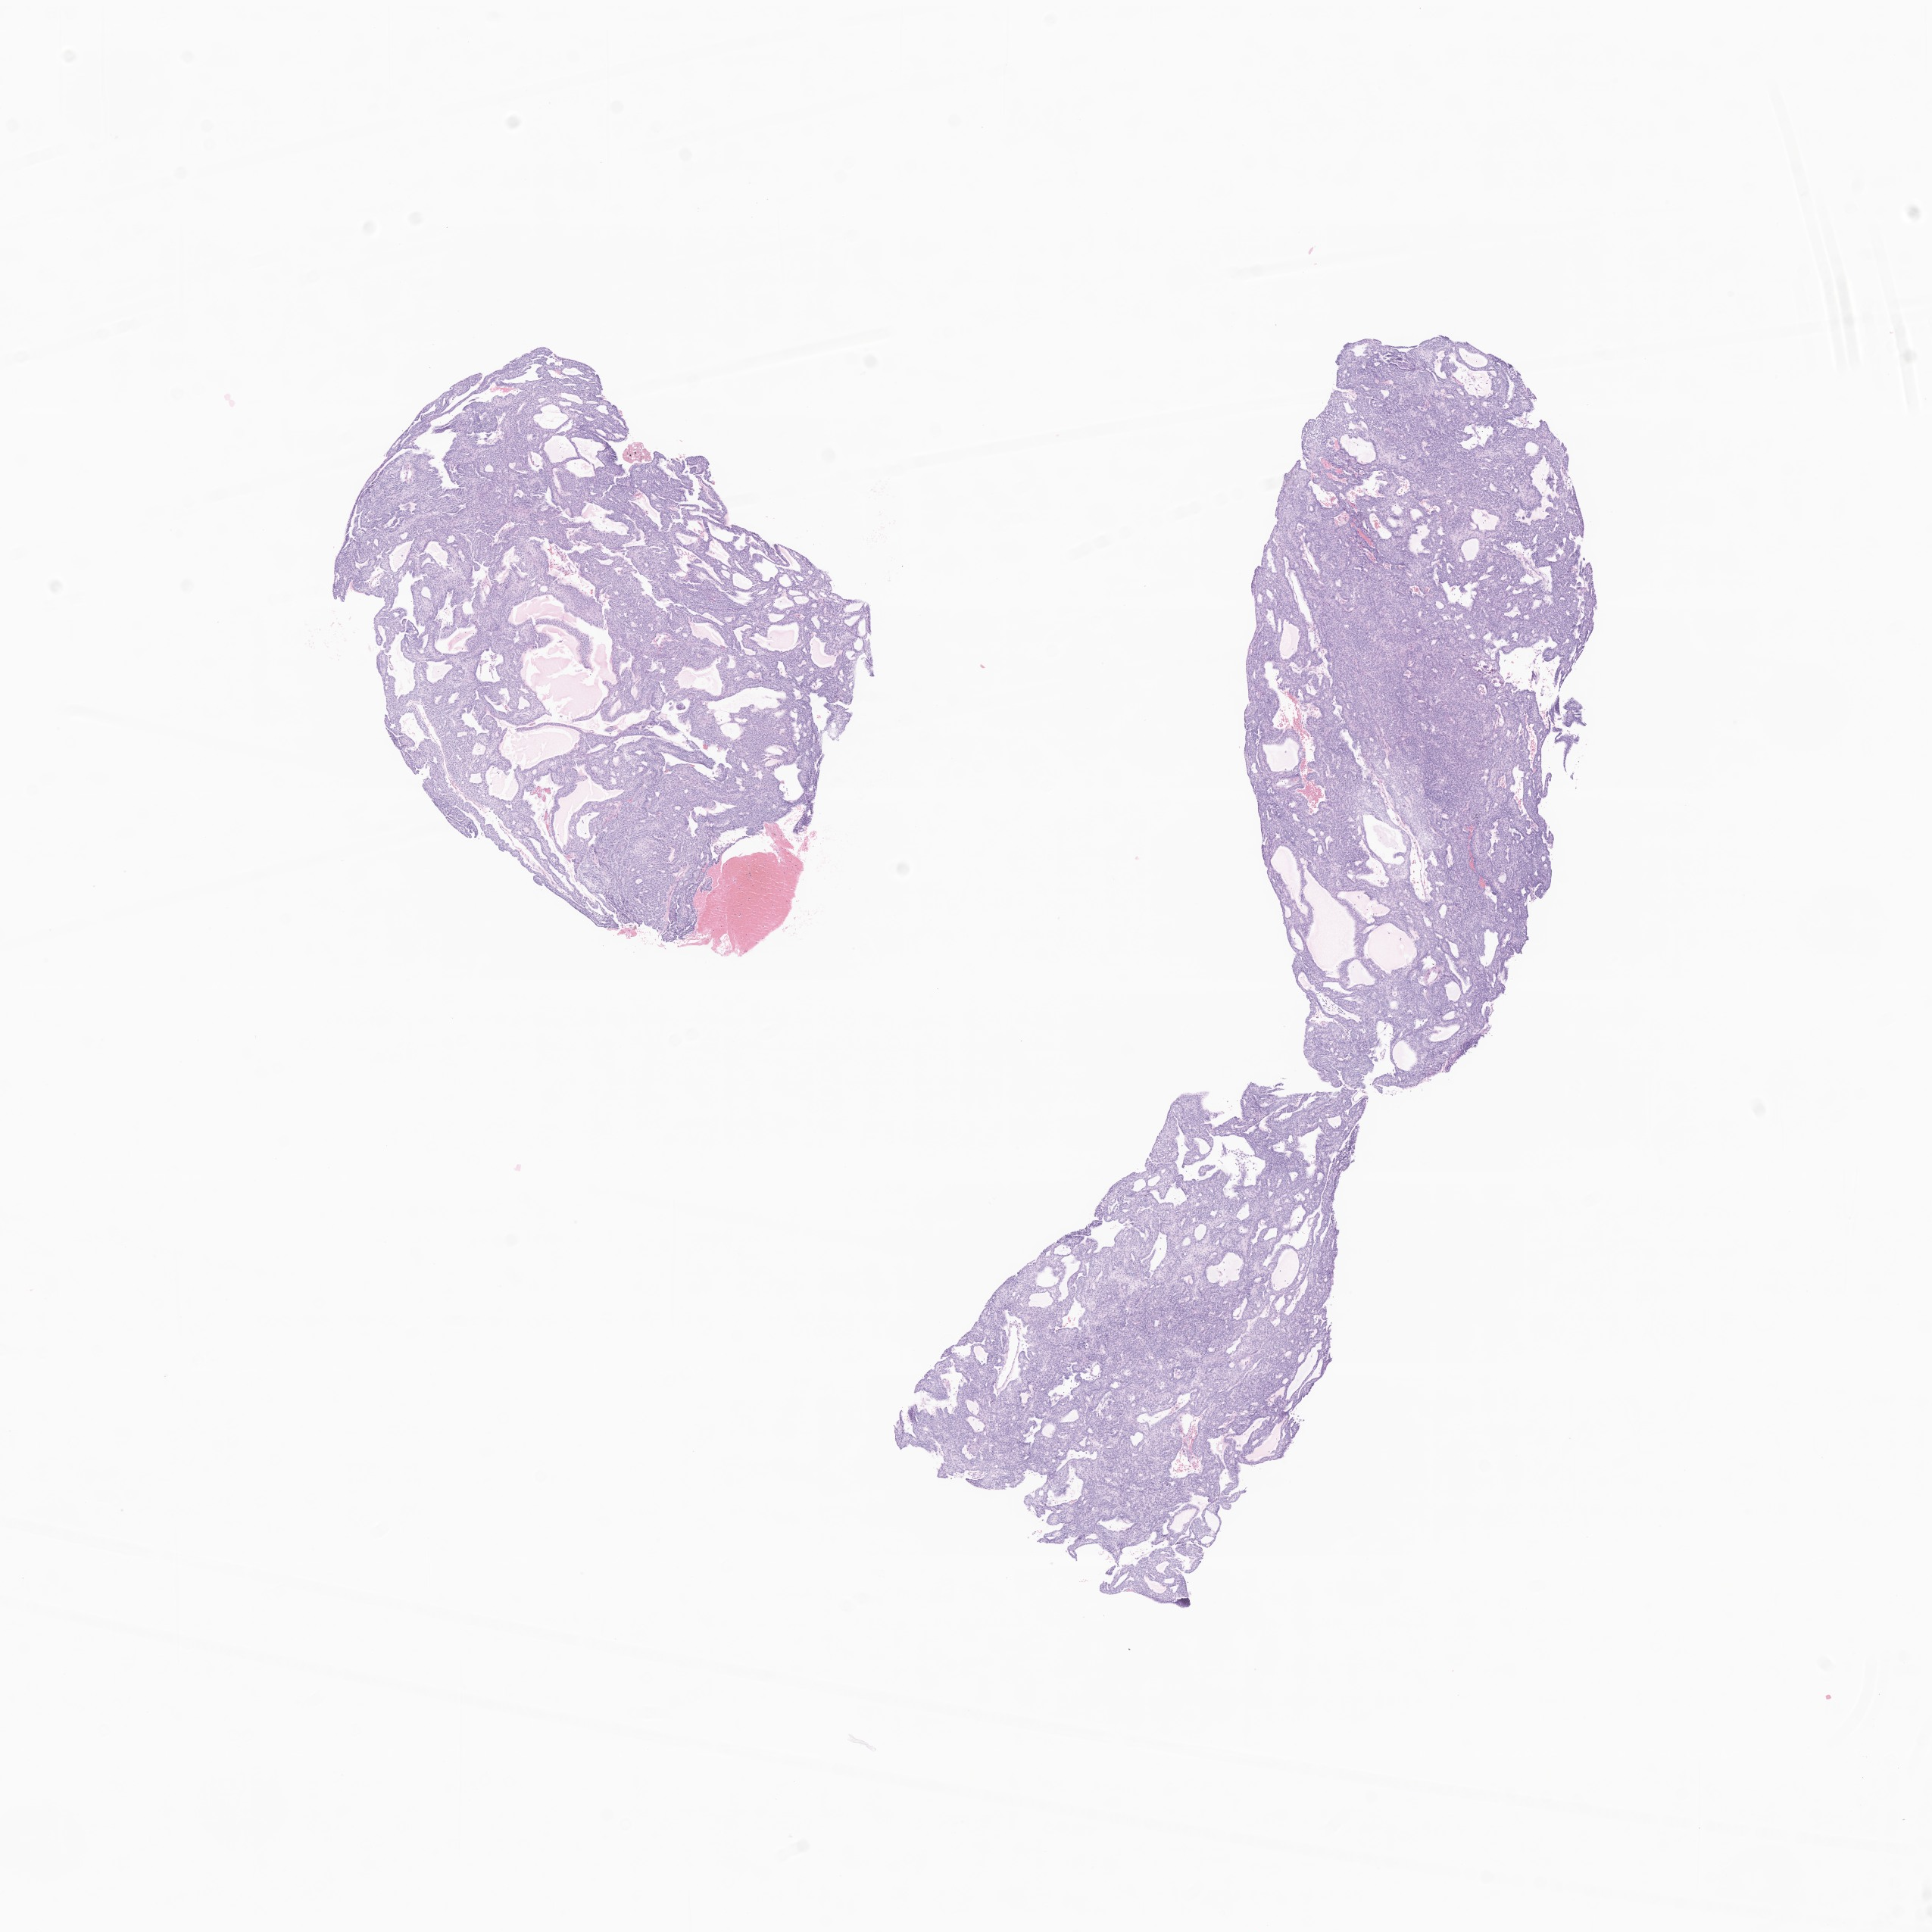
H&E whole-slide image of tumor tissue from the brain, whole scanned area (about 10.8 x 10.8 mm) shown as a low-resolution overview. FFPE section. Patient: female, age 122 months (10 years 2 months).
Recorded diagnosis: Neoplasm, uncertain whether benign or malignant.